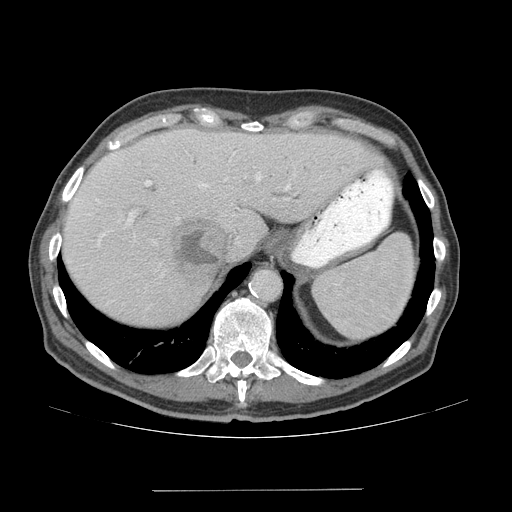
Contrast-enhanced abdominal CT (liver protocol), one axial slice; position 52 of 77 along the scan axis; reconstruction kernel STANDARD; 140 kVp; soft-tissue window (W 400 / L 40 HU); 2.5 mm slice thickness; 512 × 512 image matrix, field of view 400 × 400 mm. Case-level facts recorded for this patient, not image findings: diagnosis: hepatocellular carcinoma (patient treated with transarterial chemoembolisation; whether this scan precedes or follows treatment is not stated here); TNM stage (as recorded): Stage-IVA; Child-Pugh class: A; tumour differentiation: well differentiated; tumour nodularity: uninodular.
Structures marked on this image (semi-automatic segmentation, software-assisted and operator-edited):
- liver parenchyma outside the tumour (the mass and vessels are separate outlines, so this box may not span the whole liver): box from (x=62, y=128) to (x=376, y=326) px
- mass: (x=169, y=213)–(x=228, y=295)
- liver vessels: (x=75, y=139)–(x=290, y=246)